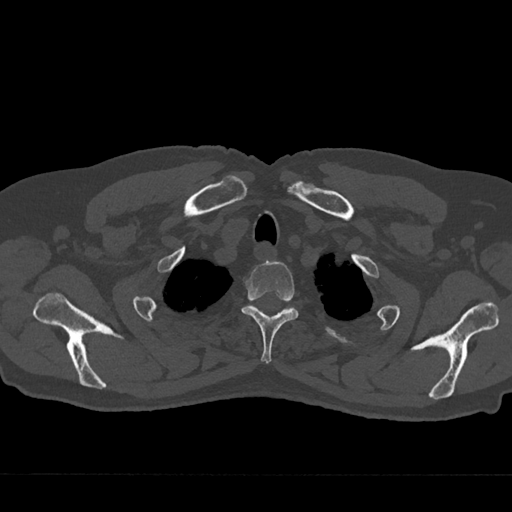
CT including the spine, one axial slice. Position 609 of 797 along the scan axis. Reconstruction kernel Br40s/3. 120 kVp. Bone window (W 1800 / L 400 HU). 0.5 mm slice thickness. 512 × 512 image matrix, field of view 377 × 377 mm. Patient: male, 75 years. Case-level facts recorded for this patient, not image findings: primary cancer: renal.
Structures marked on this image (semi-automatic segmentation, software-assisted and operator-edited):
- T2 vertebra: bounding box <241,261,299,364> (left, top, right, bottom; pixels)